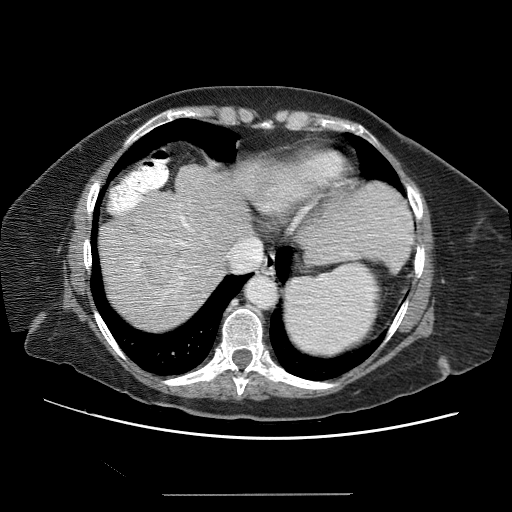
Contrast-enhanced abdominal CT (liver protocol), one axial slice. Soft-tissue window (W 400 / L 40 HU). 2.5 mm slice thickness. 512 × 512 image matrix. From the clinical record (not read from this slice): diagnosis: hepatocellular carcinoma (patient treated with transarterial chemoembolisation; whether this scan precedes or follows treatment is not stated here); TNM stage (as recorded): Stage-IIIB; Child-Pugh class: A; tumour nodularity: uninodular.
Outlined on this slice (semi-automatically segmented with operator editing):
- liver parenchyma outside the tumour (the mass and vessels are separate outlines, so this box may not span the whole liver): bounding box (x1, y1, x2, y2) in pixels: (100, 164, 248, 322)
- mass: (133, 239, 183, 286)
- liver vessels: (117, 189, 213, 298)